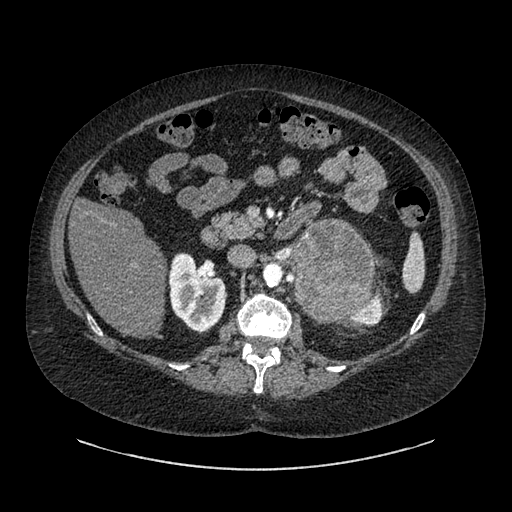
Contrast-enhanced abdominal CT, one axial slice. Position 530 of 769 along the scan axis. Reconstruction kernel SOFT. 120 kVp. Soft-tissue window (W 400 / L 40 HU). 0.62 mm slice thickness. 512 × 512 image matrix, field of view 460 × 460 mm. Female patient, age 61 years. Case-level facts recorded for this patient, not image findings: diagnosis: adrenocortical carcinoma; tumour side: left adrenal; tumour size at pathology: 13 cm; Ki-67 index: 79 %; stage (as recorded): 2.
Outlined on this slice (semi-automatically segmented with operator editing):
- mass: bounding box [x1, y1, x2, y2] px = [294, 221, 373, 320]